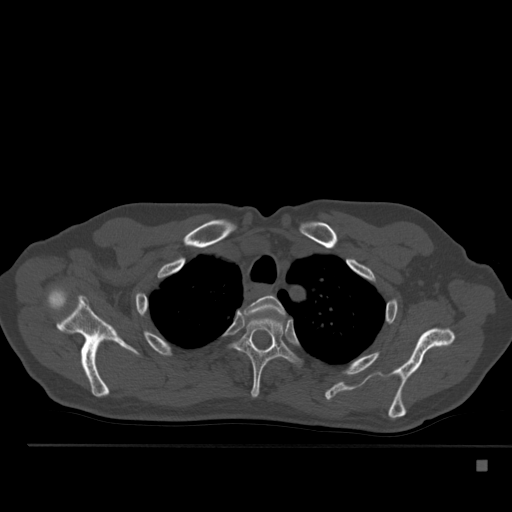
CT including the spine, one axial slice. Slice 399 of 517 in the series (ordered by position). Bone window (W 1800 / L 400 HU). 1.5 mm slice thickness. 512 × 512 image matrix, field of view 408 × 408 mm. Male patient, age 70 years. Case-level facts recorded for this patient, not image findings: primary cancer: renal.
Annotated regions visible in this slice (semi-automatic segmentation, software-assisted and operator-edited):
- T2 vertebra: bounding box [x1, y1, x2, y2] px = [244, 295, 285, 316]
- T3 vertebra: [233, 318, 297, 398]